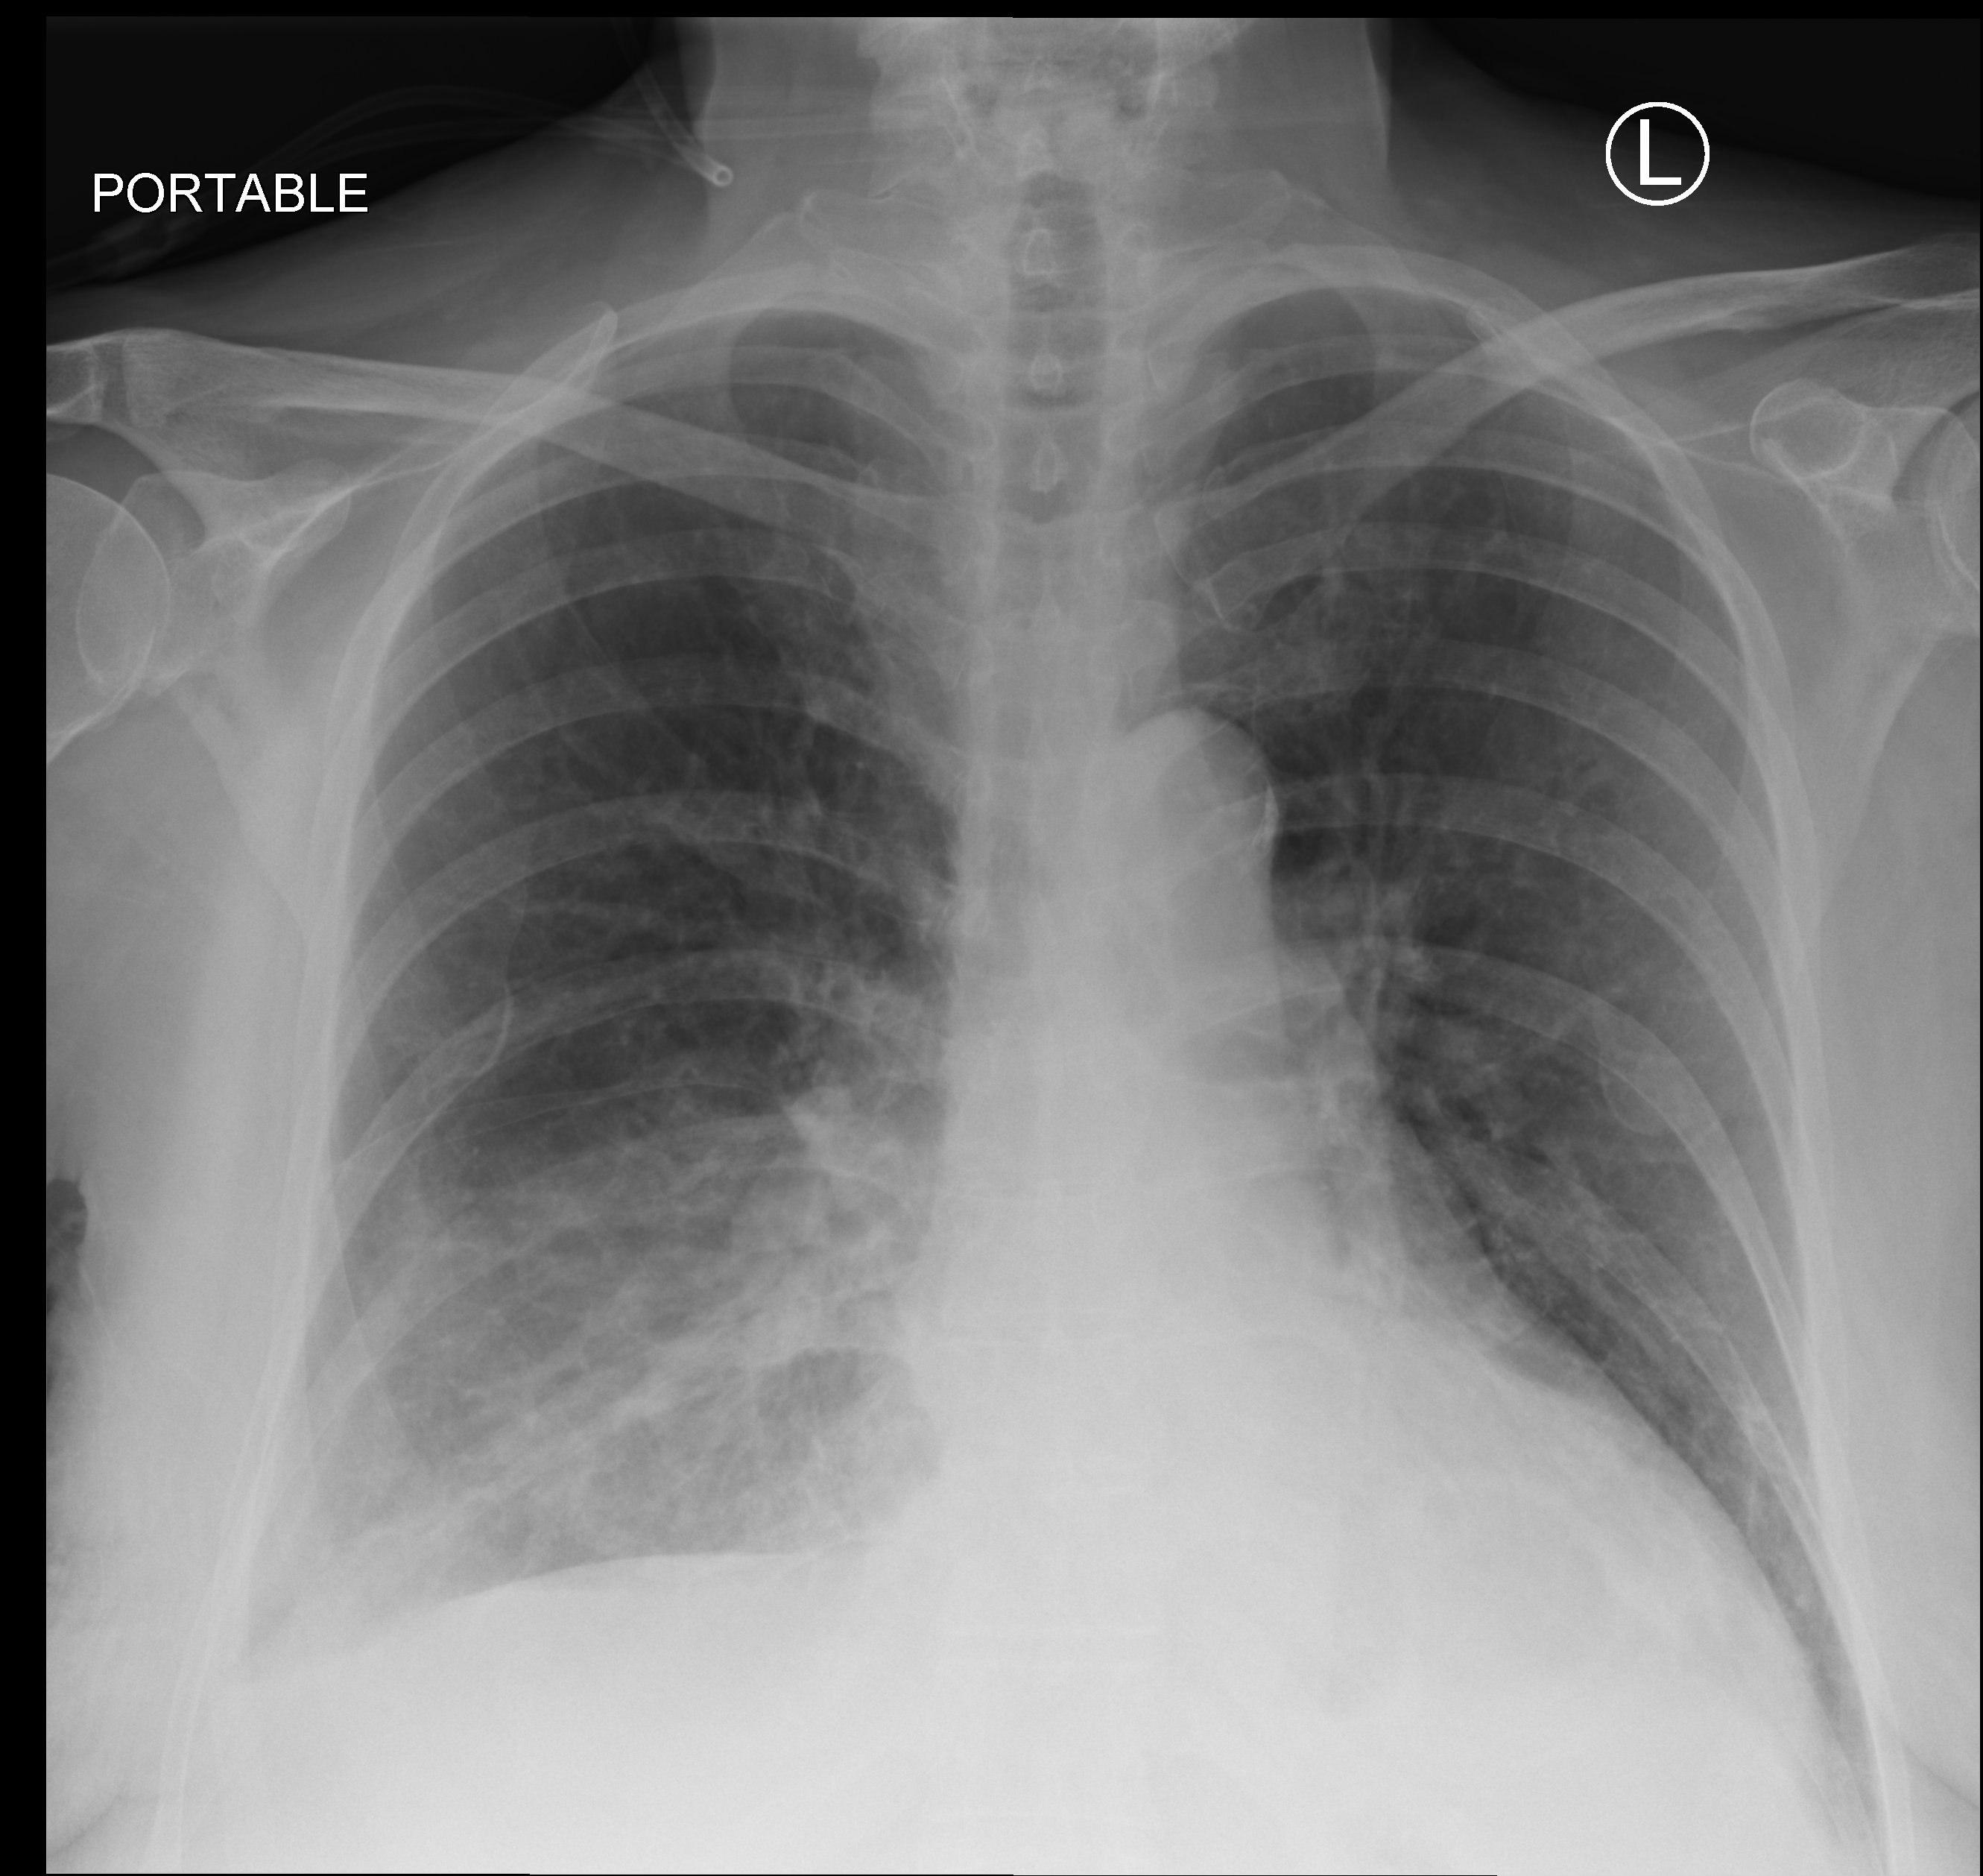
Chest X-ray (portable); anteroposterior (AP) projection. Female patient hospitalised with COVID-19, age 18–59 years.
Hospital-stay facts (about this admission, not read from this image; timing relative to this image not recorded):
- mechanically ventilated during this hospital stay: no